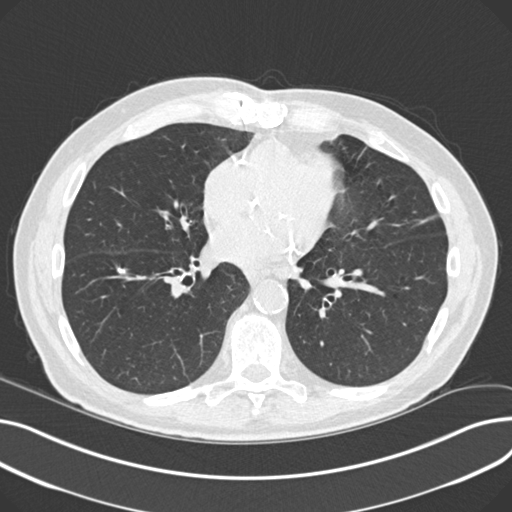
Low-dose screening chest CT, one axial slice. Slice 95 of 230 in the series (ordered by position). 120 kVp. Lung window (W 1500 / L -600 HU). 512 × 512 image matrix.
Outlined on this slice (manually delineated by an expert):
- lesion 2 (tumor, lower lobe of right lung): box from (x=117, y=268) to (x=126, y=275) px